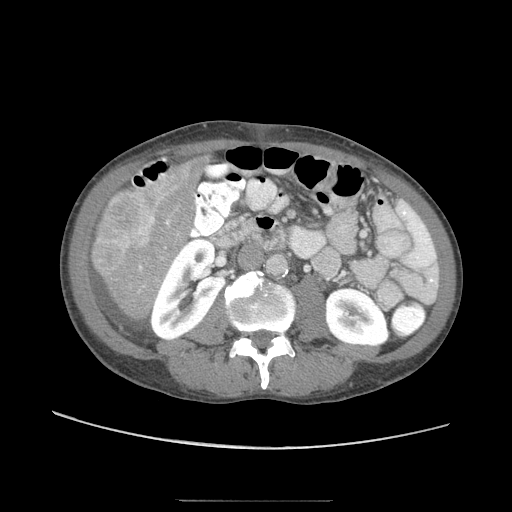
Contrast-enhanced abdominal CT (liver protocol), one axial slice; position 14 of 103 along the scan axis; reconstruction kernel STANDARD; 120 kVp; soft-tissue window (W 400 / L 40 HU); 2.5 mm slice thickness; 512 × 512 image matrix, field of view 380 × 380 mm. Case-level facts recorded for this patient, not image findings: diagnosis: hepatocellular carcinoma (patient treated with transarterial chemoembolisation; whether this scan precedes or follows treatment is not stated here); TNM stage (as recorded): Stage-IIIA; Child-Pugh class: A.
Annotated regions visible in this slice (semi-automatic segmentation, software-assisted and operator-edited):
- liver parenchyma outside the tumour (the mass and vessels are separate outlines, so this box may not span the whole liver): bounding box <90,154,210,322> (left, top, right, bottom; pixels)
- mass: <92,185,157,274>